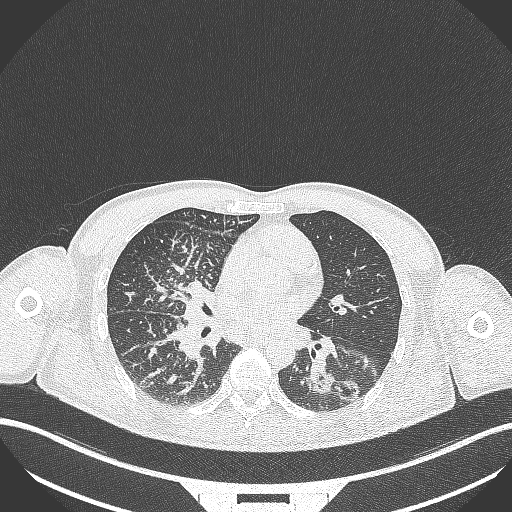
Chest CT, one axial slice; position 155 of 348 along the scan axis; reconstruction kernel B70f; 120 kVp; lung window (W 1500 / L -600 HU); 1 mm slice thickness; 512 × 512 image matrix, field of view 400 × 400 mm. Patient: male, 49 years. Case-level facts recorded for this patient, not image findings: clinical TNM (as recorded): T2b N1 M0.
Structures marked on this image (rectangle marked by the reading radiologist):
- lung tumour (recorded histology: adenocarcinoma): bounding box (x1, y1, x2, y2) in pixels: (300, 358, 366, 407)